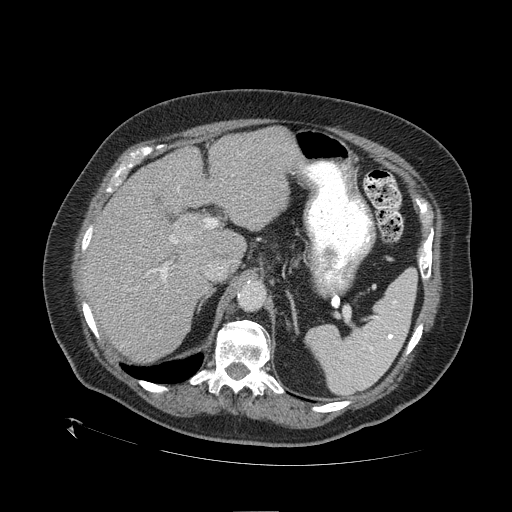
Contrast-enhanced abdominal CT (liver protocol), one axial slice; slice 73 of 109 in the series (ordered by position); 120 kVp; one of 2 acquisitions stored at this slice position; soft-tissue window (W 400 / L 40 HU); 512 × 512 image matrix. Case-level facts recorded for this patient, not image findings: diagnosis: hepatocellular carcinoma (patient treated with transarterial chemoembolisation; whether this scan precedes or follows treatment is not stated here); TNM stage (as recorded): Stage-I; Child-Pugh class: A; tumour nodularity: uninodular.
Outlined on this slice (semi-automatically segmented with operator editing):
- liver parenchyma outside the tumour (the mass and vessels are separate outlines, so this box may not span the whole liver): bounding box <82,128,300,360> (left, top, right, bottom; pixels)
- mass: <176,216,205,246>
- liver vessels: <147,187,179,282>